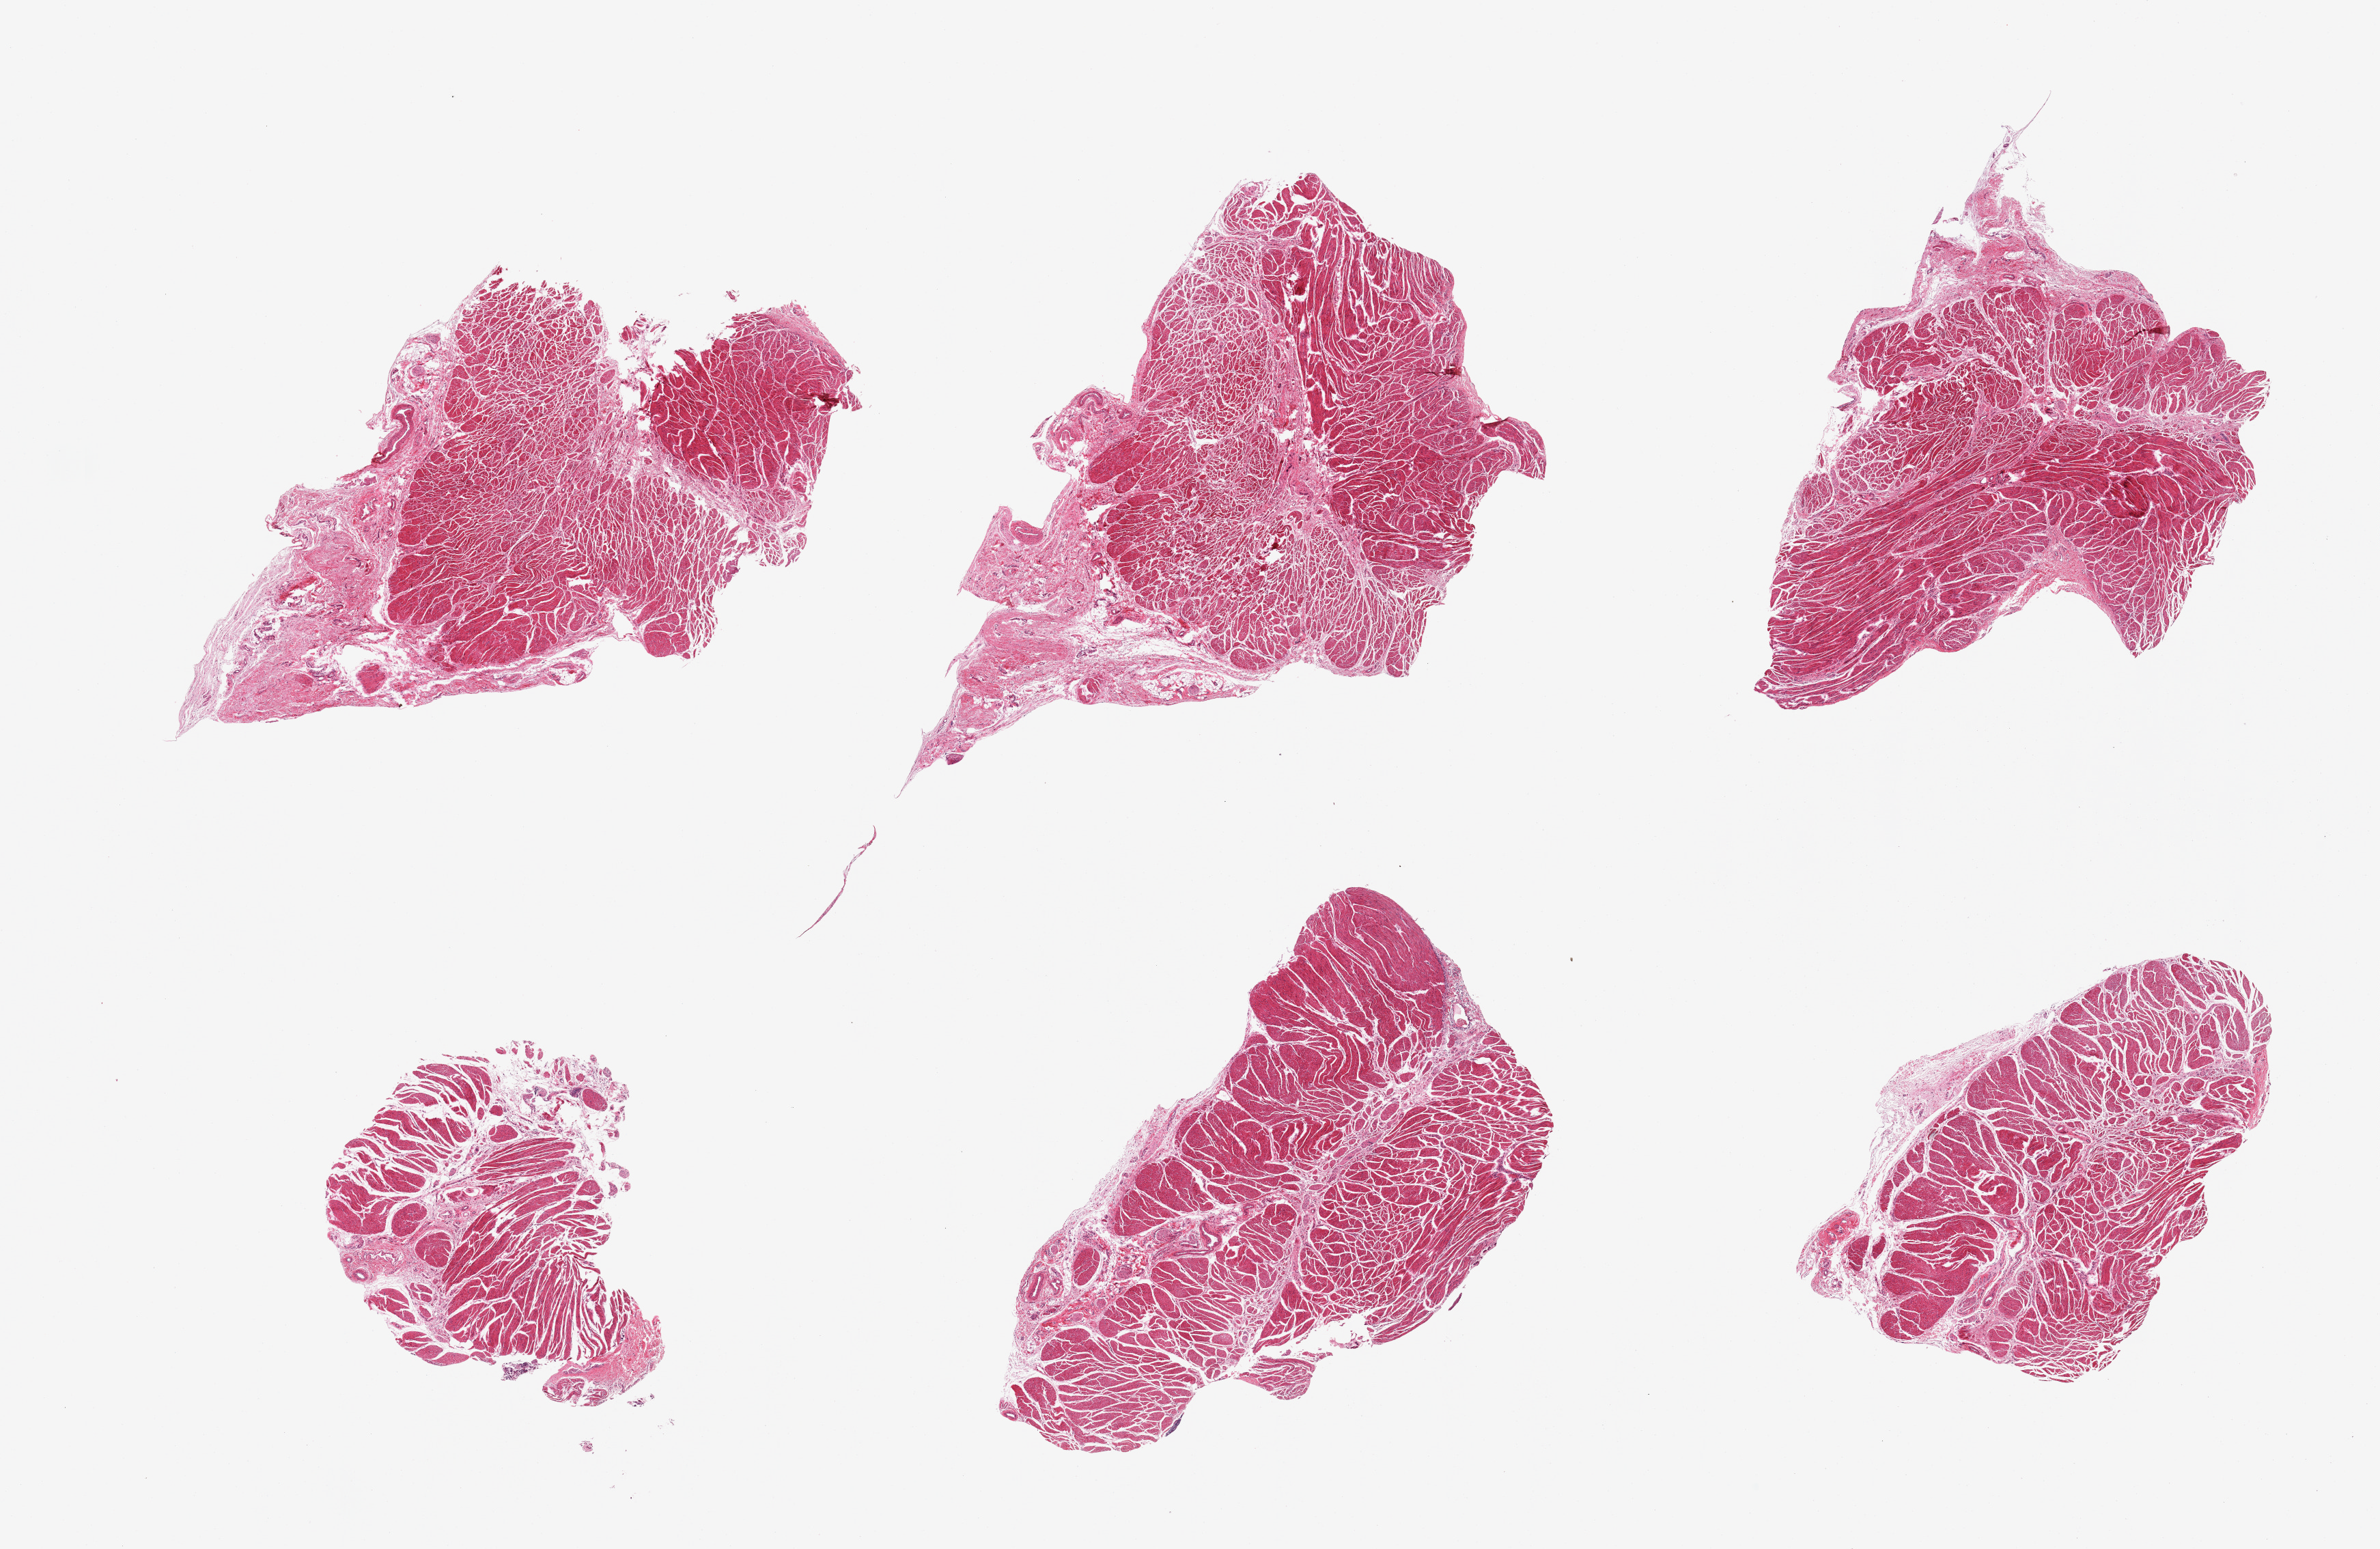
Haematoxylin and eosin whole-slide image — low-resolution overview of the scanned area, about 27.6 x 17.9 mm, PAXgene-fixed paraffin-embedded (PFPE) section, sampled site (target tissue): gastroesophageal junction, tissue donor sample.
Reviewer comment on this tissue sample: 6 pieces; well trimmed.